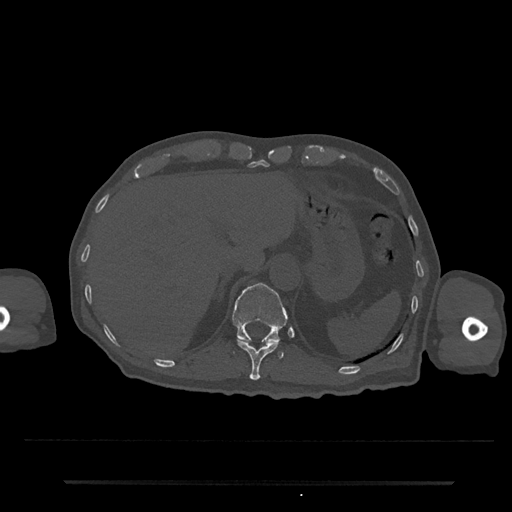
CT including the spine, one axial slice. Position 227 of 797 along the scan axis. Bone window (W 1800 / L 400 HU). 0.5 mm slice thickness. 512 × 512 image matrix. Male patient, age 74 years. From the clinical record (not read from this slice): primary cancer: prostate.
Structures marked on this image (semi-automatically segmented with operator editing):
- T11 vertebra: box from (x=237, y=338) to (x=279, y=380) px
- T12 vertebra: (x=232, y=283)–(x=288, y=358)